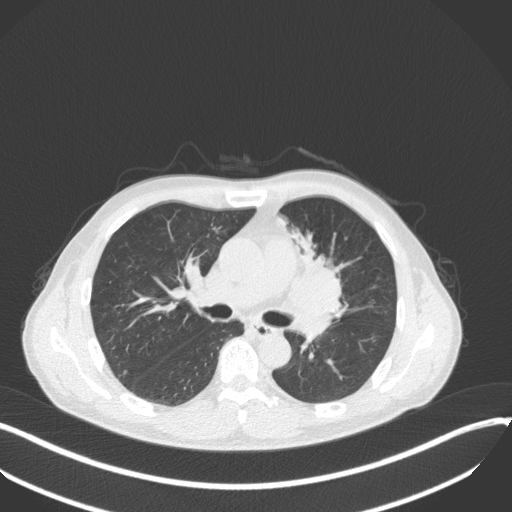
Chest CT, one axial slice; reconstruction kernel B31f; lung window (W 1500 / L -600 HU); 1 mm slice thickness; 512 × 512 image matrix. Patient: male, 56 years. From the clinical record (not read from this slice): clinical TNM (as recorded): T2a N0 M0.
Annotated regions visible in this slice (bounding box drawn by a radiologist):
- lung tumour (recorded histology: squamous cell carcinoma): bounding box [x1, y1, x2, y2] px = [286, 227, 348, 320]